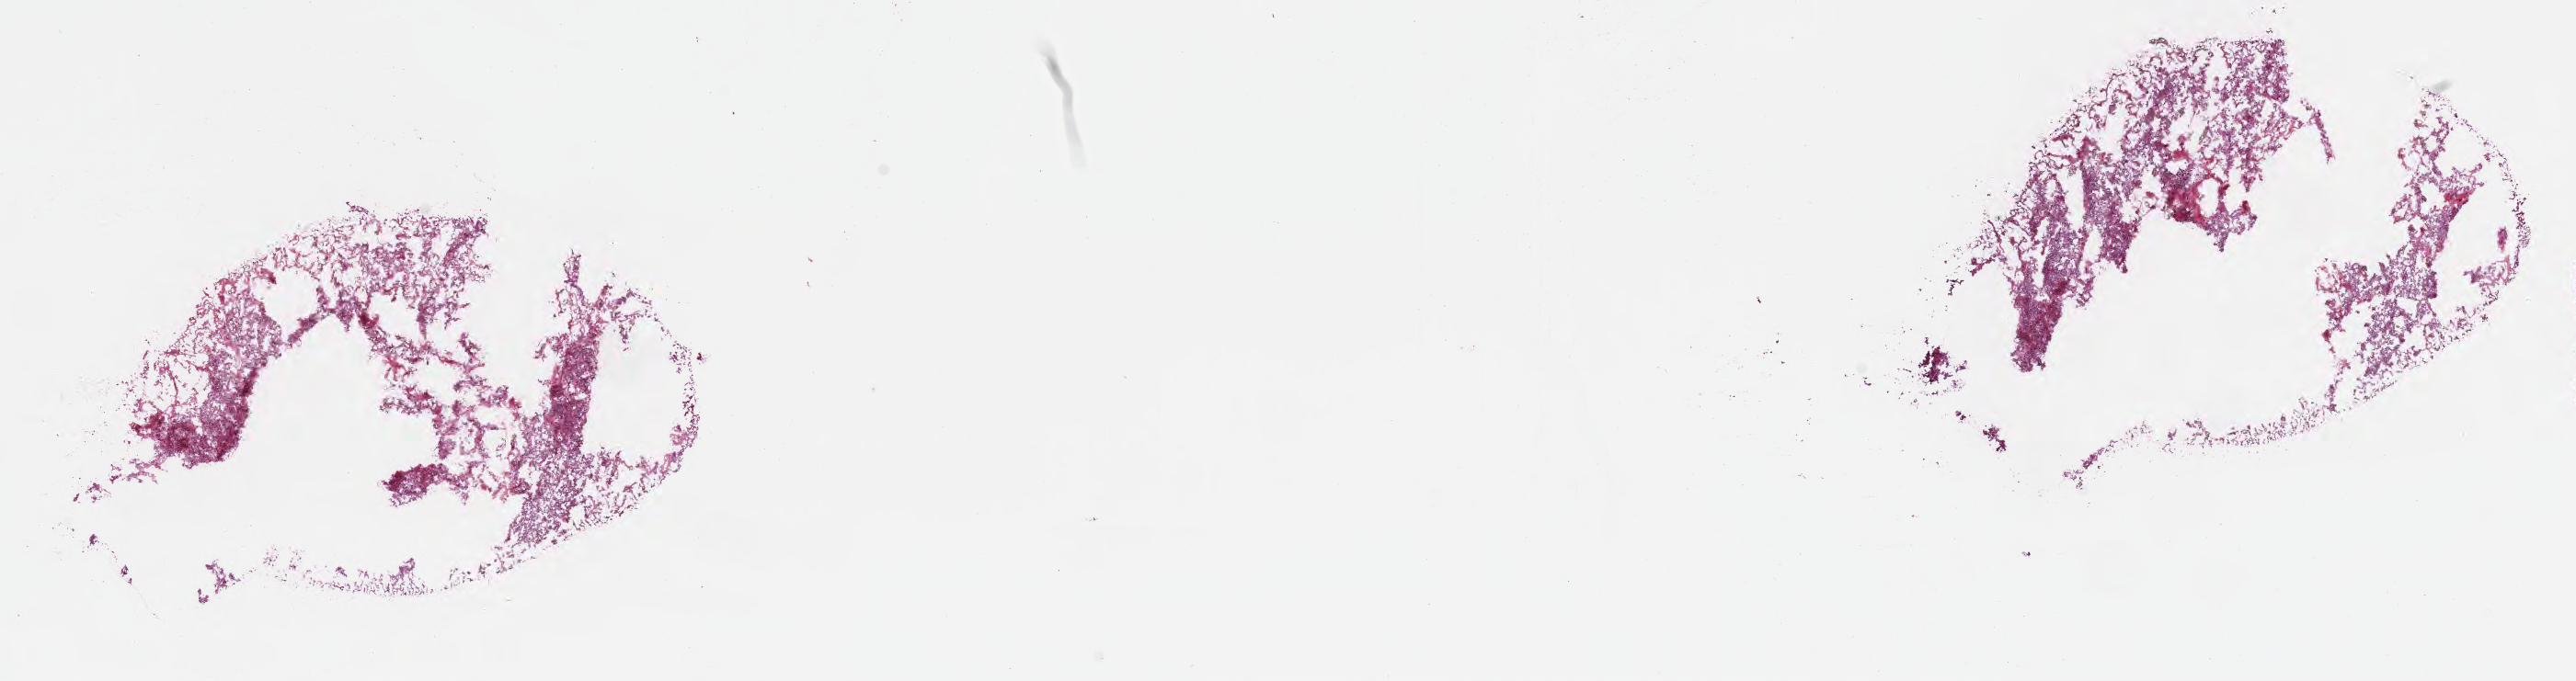
Haematoxylin and eosin whole-slide image, a low-resolution overview of the entire scanned area, about 22.7 x 6.0 mm. Frozen section. Specimen: primary tumor. Site: kidney. Male, age 63 years at initial diagnosis. Composition of this section per pathologist review: tumor cells 60%, tumor nuclei 92%, stromal cells 20%, necrosis 20%, normal cells 0%. Inflammatory infiltration, as recorded: lymphocyte infiltration 5%, monocyte infiltration 0%, neutrophil infiltration 0%.
Diagnosis: Renal cell carcinoma, chromophobe type. AJCC pathologic stage: Stage II. Section: bottom of the tissue portion.